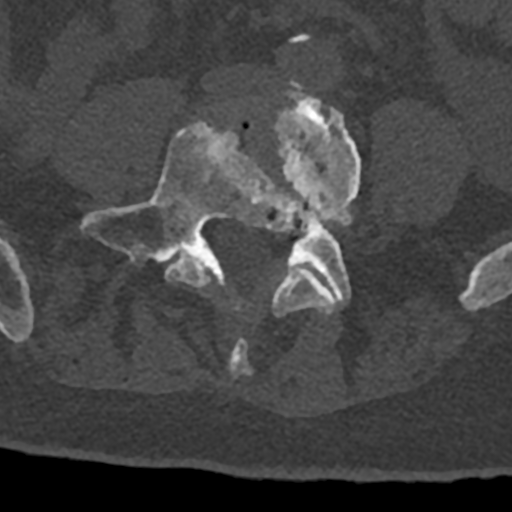
CT including the spine, one axial slice; bone window (W 1800 / L 400 HU); 0.5 mm slice thickness; 512 × 512 image matrix. Patient: male, 74 years. Case-level facts recorded for this patient, not image findings: primary cancer: renal.
Annotated regions visible in this slice (semi-automatic segmentation, software-assisted and operator-edited):
- L4 vertebra: bounding box (x1, y1, x2, y2) in pixels: (165, 83, 362, 376)
- L5 vertebra: (81, 122, 351, 308)